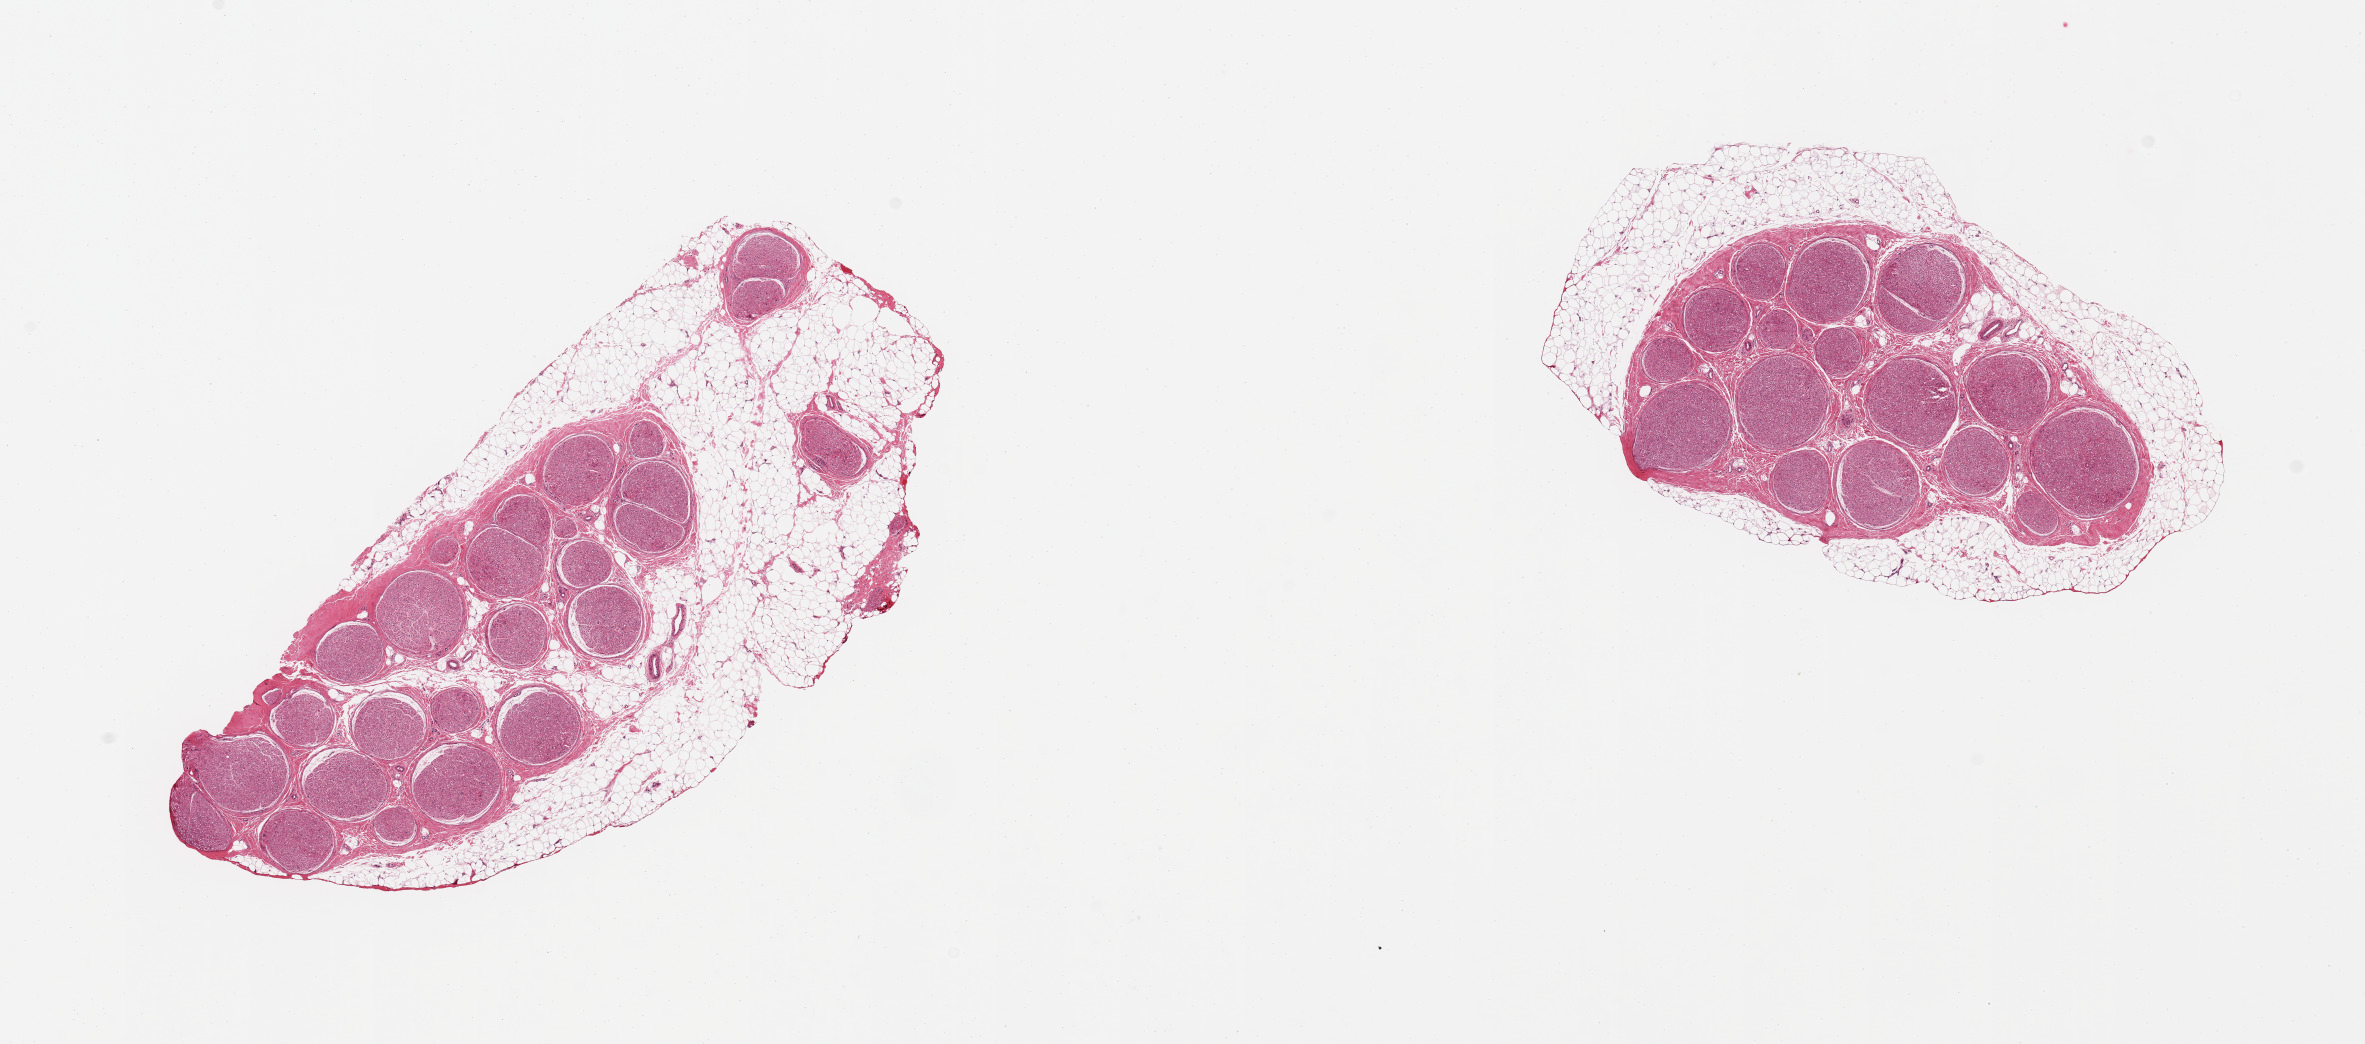
Digitized H&E-stained section — low-resolution overview of the scanned area, about 18.7 x 8.3 mm, PAXgene-fixed, paraffin-embedded tissue, section of tibial nerve (target tissue), donor tissue sample. Donor: female.
Reviewer comment on this tissue sample: 2 pieces, rims of adherent fat, 1-2mm.